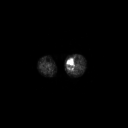
FDG PET of an extremity soft-tissue mass (from a PET/CT study), one axial slice. Position 132 of 223 along the scan axis. 128 × 128 image matrix. Patient: female, 70 years. From the clinical record (not read from this slice): histological type: extraskeletal high grade osteogenic sarcoma; grade: high; site of the primary tumour: left calf.
Outlined on this slice (expert contour drawn on MRI and transferred to this co-registered scan by the dataset authors):
- gross tumour volume (mass): box from (x=67, y=61) to (x=73, y=68) px